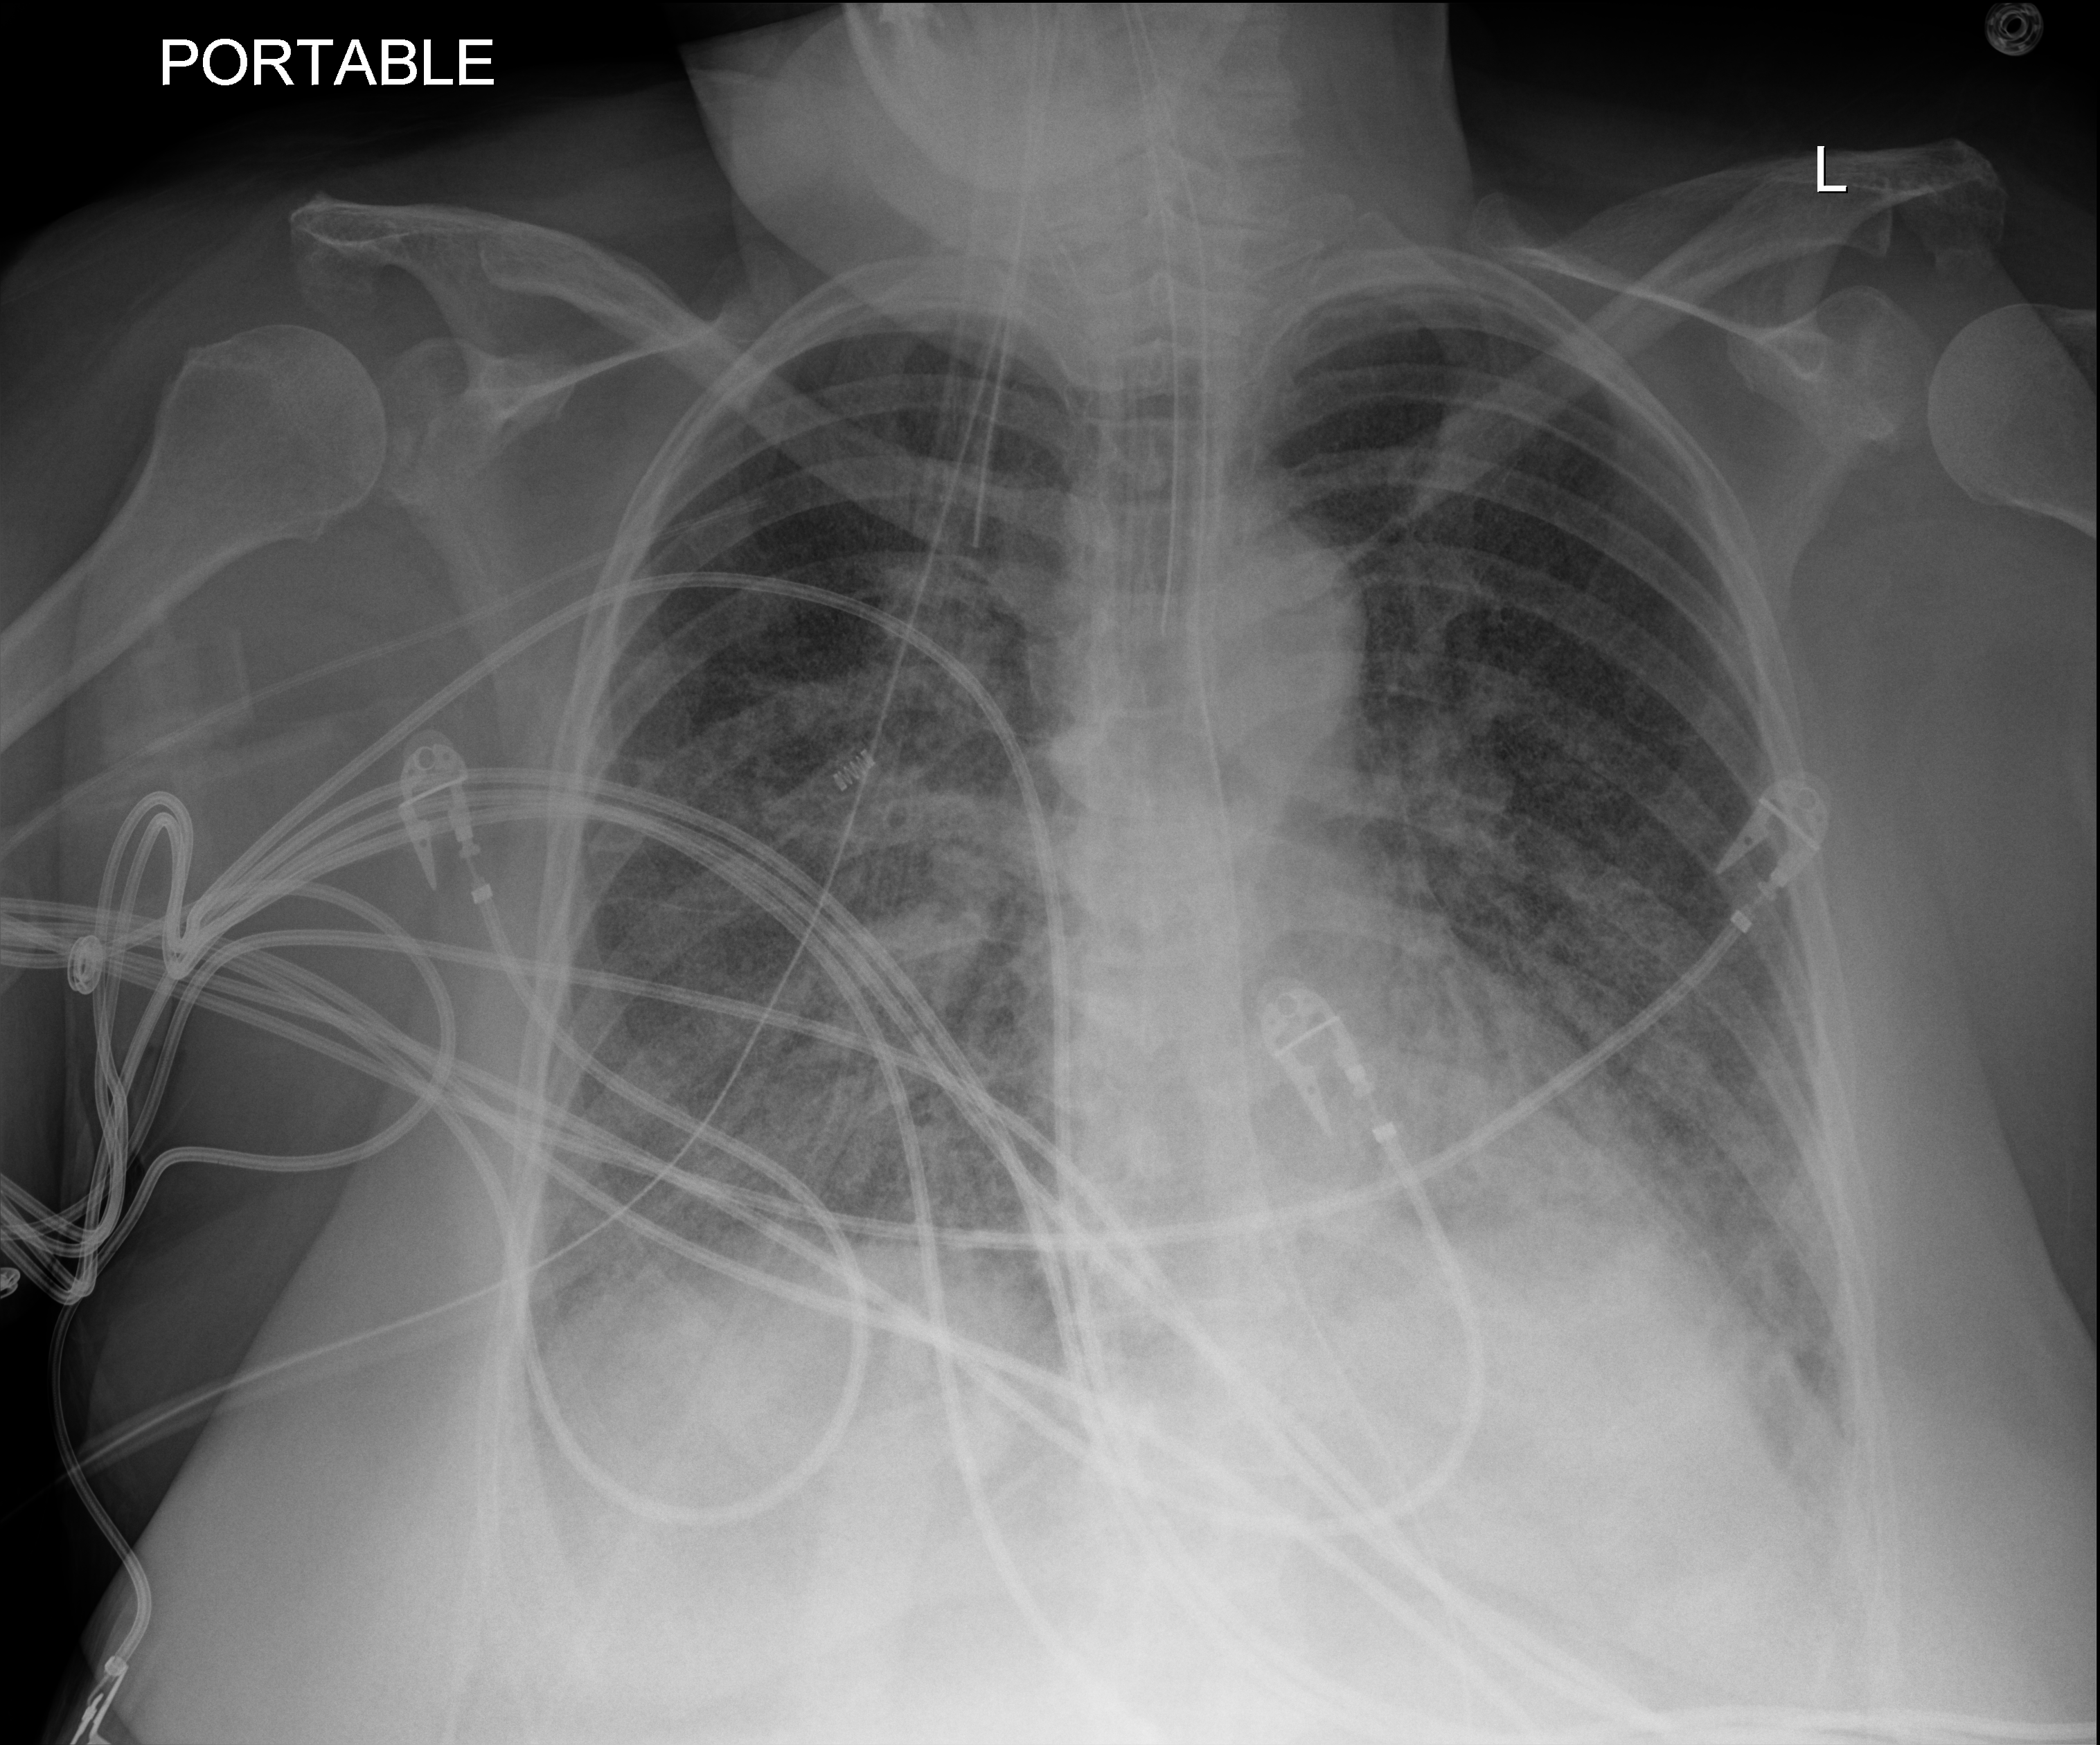
Bedside chest radiograph (digital radiography), anteroposterior (AP) projection. Female patient hospitalised with COVID-19, age 60–74 years.
Admission-level facts for this patient (not findings on this image; timing relative to this image not recorded): admitted to intensive care during this hospital stay: yes.